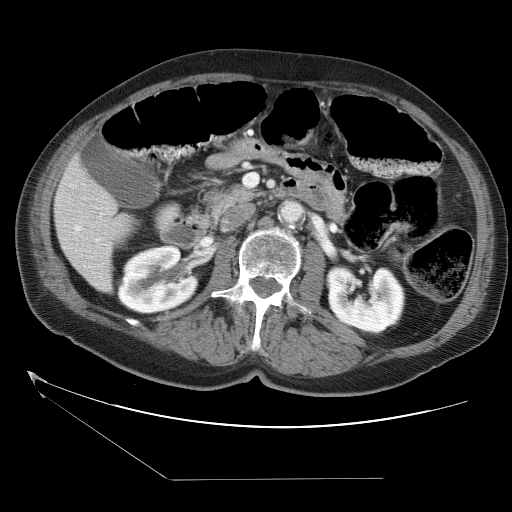
Contrast-enhanced abdominal CT (liver protocol), one axial slice; slice 10 of 38 in the series (ordered by position); 120 kVp; one of 2 acquisitions stored at this slice position; soft-tissue window (W 400 / L 40 HU); 5 mm slice thickness; 512 × 512 image matrix. Case-level facts recorded for this patient, not image findings: diagnosis: hepatocellular carcinoma (patient treated with transarterial chemoembolisation; whether this scan precedes or follows treatment is not stated here); TNM stage (as recorded): Stage-II; Child-Pugh class: A; tumour differentiation: moderately differentiated.
Outlined on this slice (semi-automatic segmentation, software-assisted and operator-edited):
- liver parenchyma outside the tumour (the mass and vessels are separate outlines, so this box may not span the whole liver): bounding box [x1, y1, x2, y2] px = [54, 154, 130, 290]
- liver vessels: [74, 225, 99, 242]